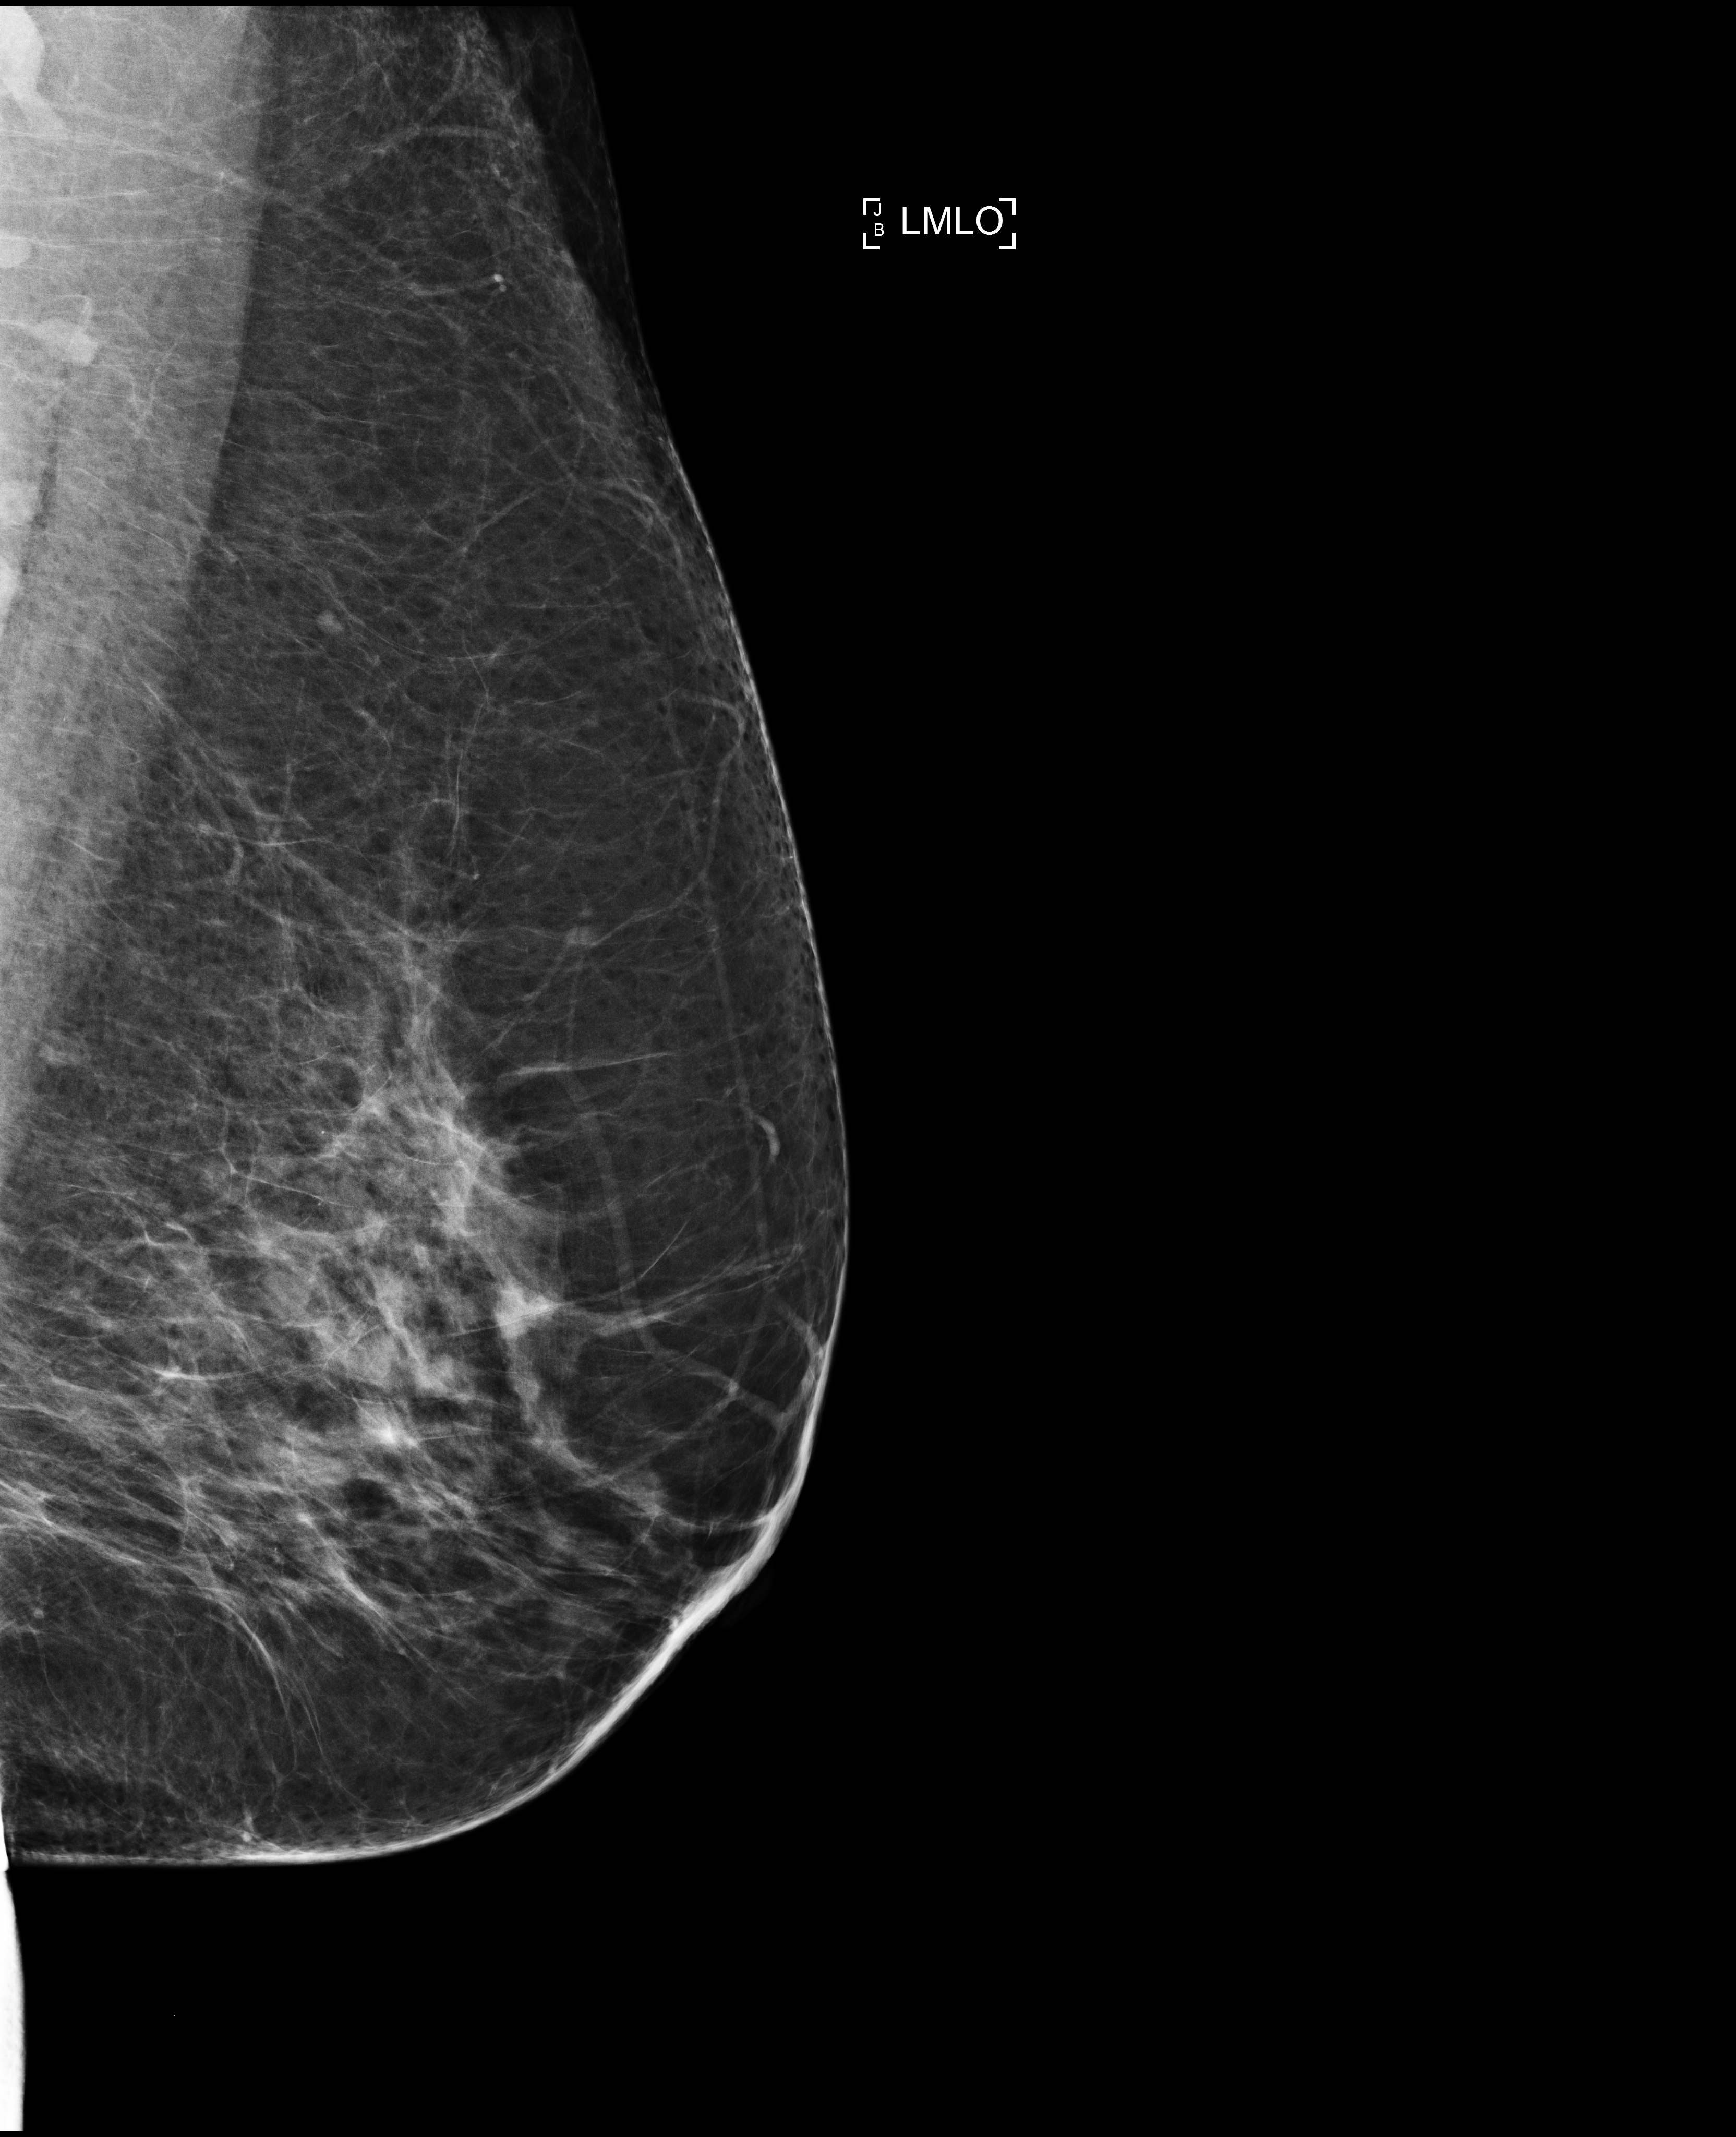
Digital mammogram (FFDM); left breast; medio-lateral oblique projection; screening examination; compressed breast thickness 81 mm. Female patient, age 55 years.
Breast density at the screening exam (both breasts): heterogeneously dense (BI-RADS density category c). Final BI-RADS category for the screening round (tomosynthesis exam, both breasts): category 1. Recall: no recall after this screen.